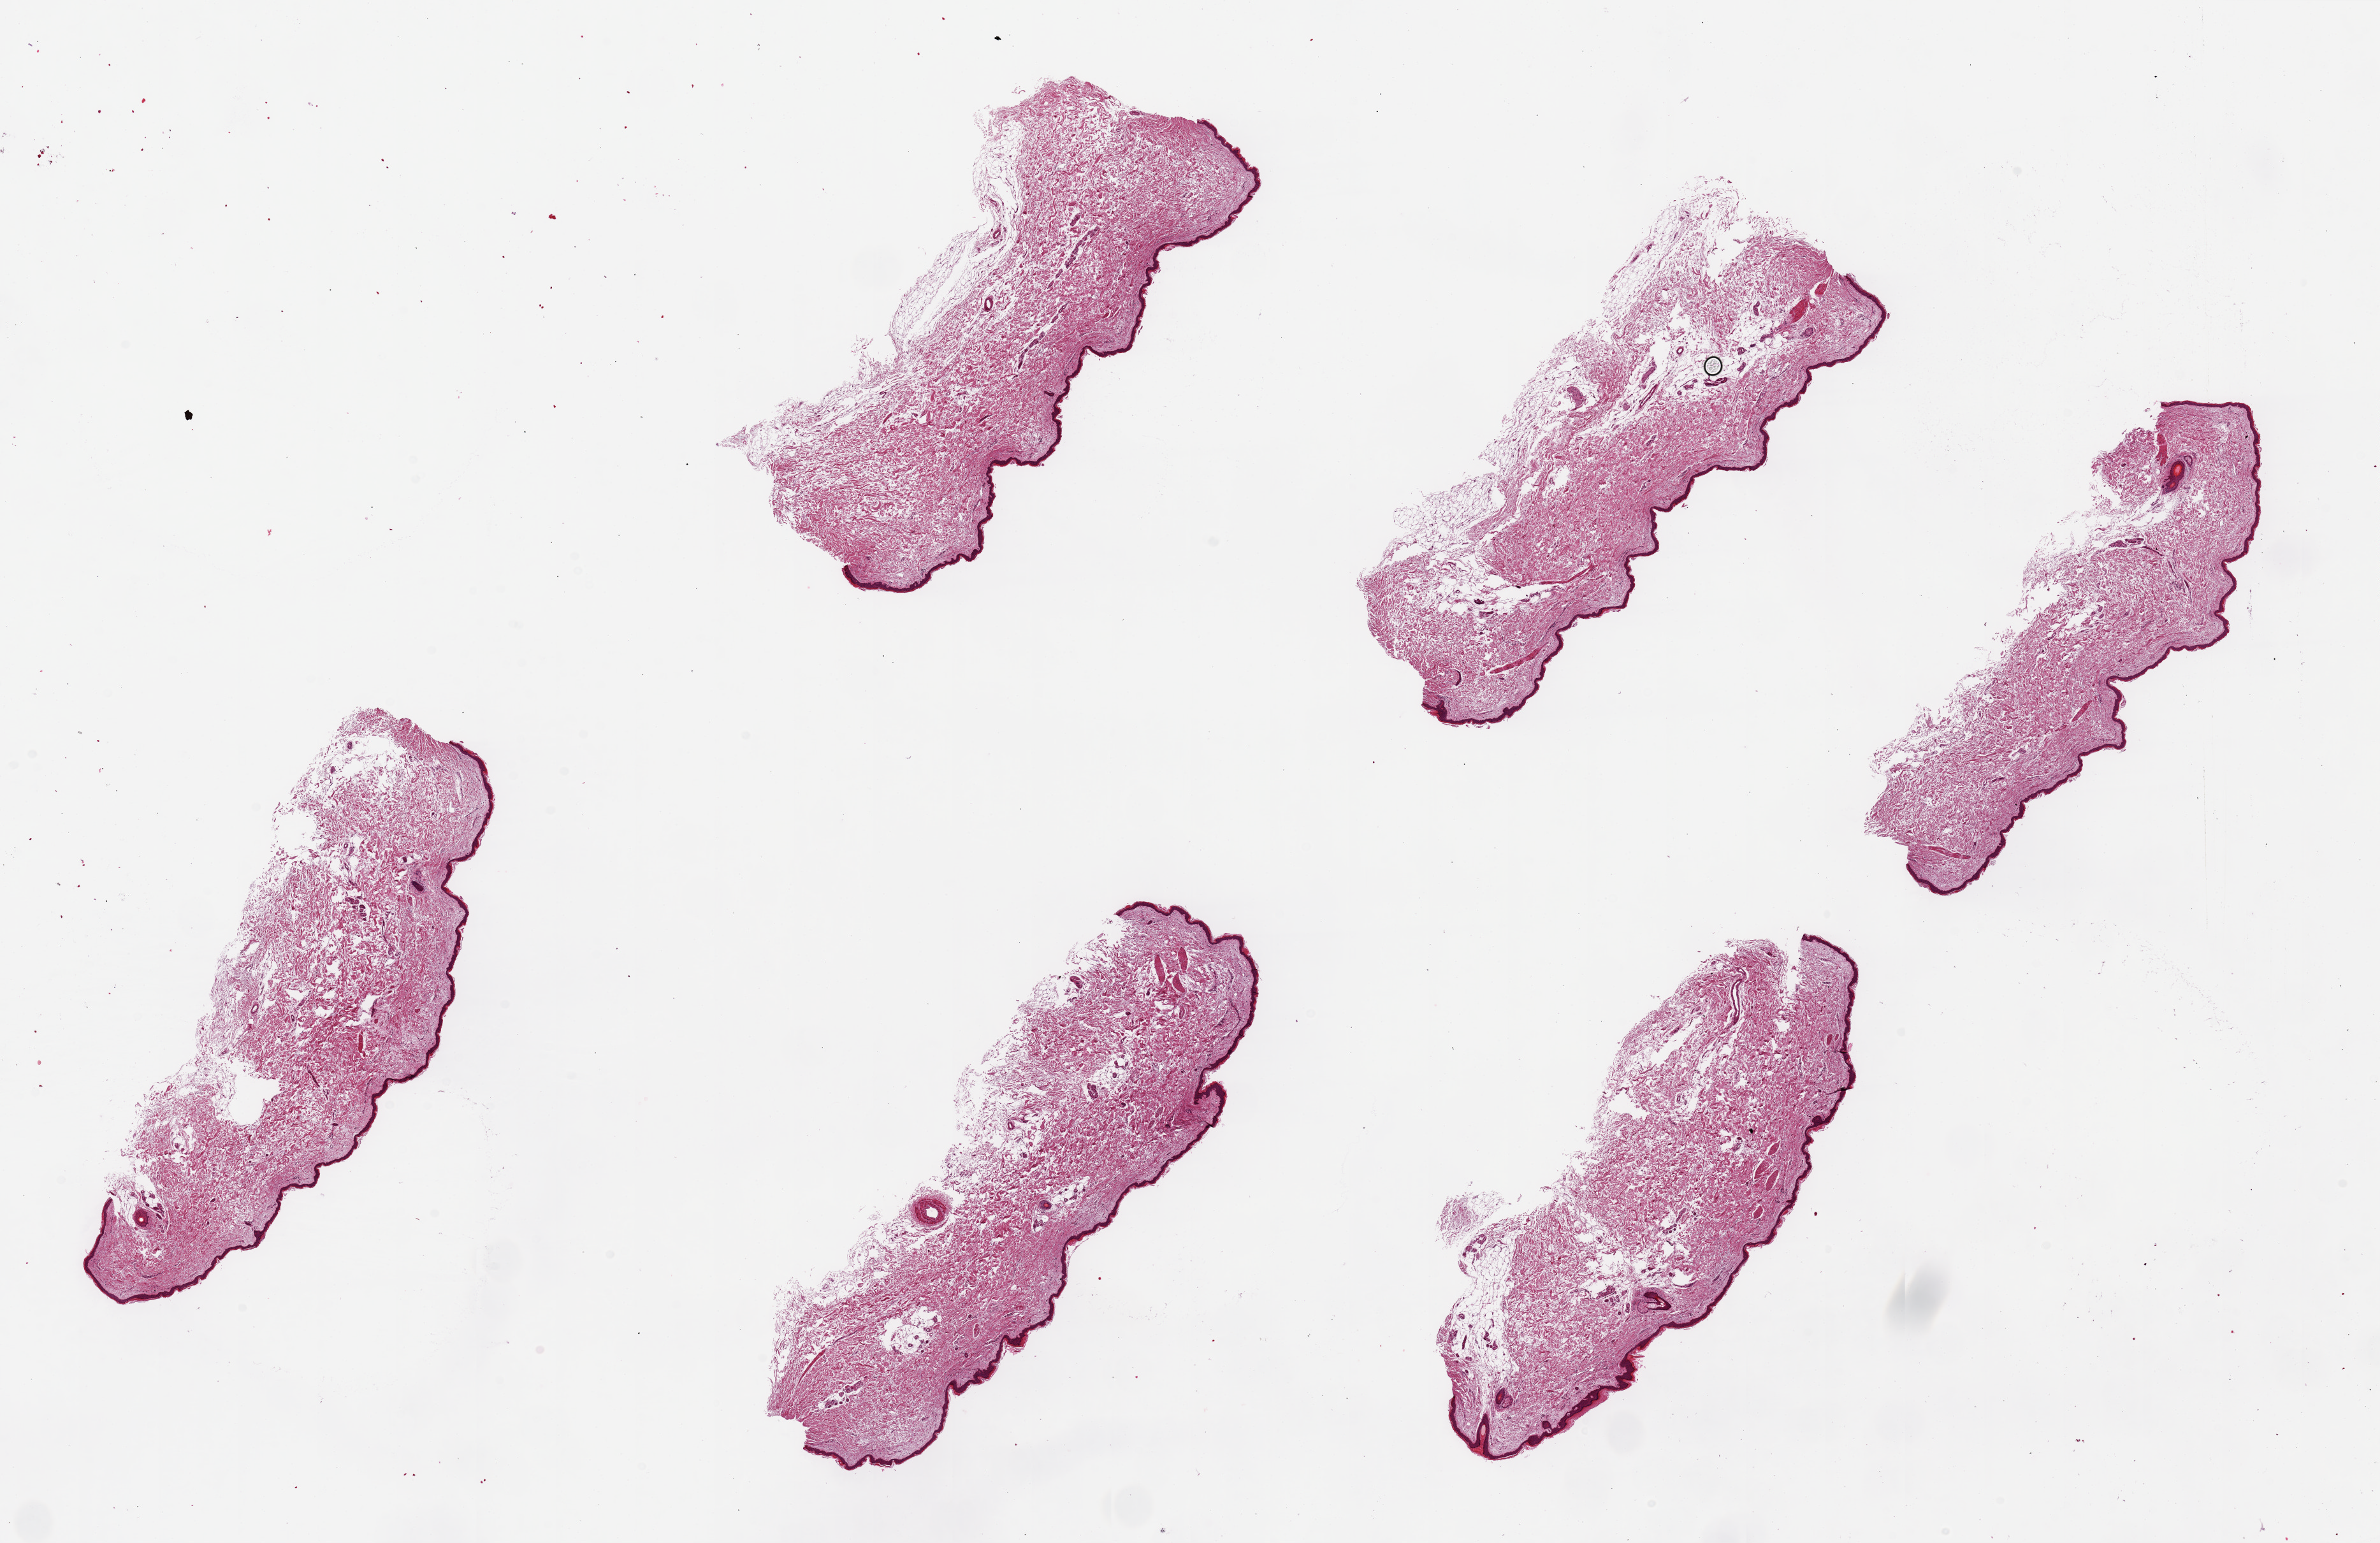
Digitized H&E-stained section, whole scanned area (about 29.5 x 19.1 mm) shown as a low-resolution overview; PAXgene-fixed, paraffin-embedded tissue; sampled site (target tissue): skin of lower leg; tissue donor sample. Donor sex: male.
Review note (as recorded): 6 pieces ~8x3.5mm. Squamous epithelium is ~ 2% of thickness.